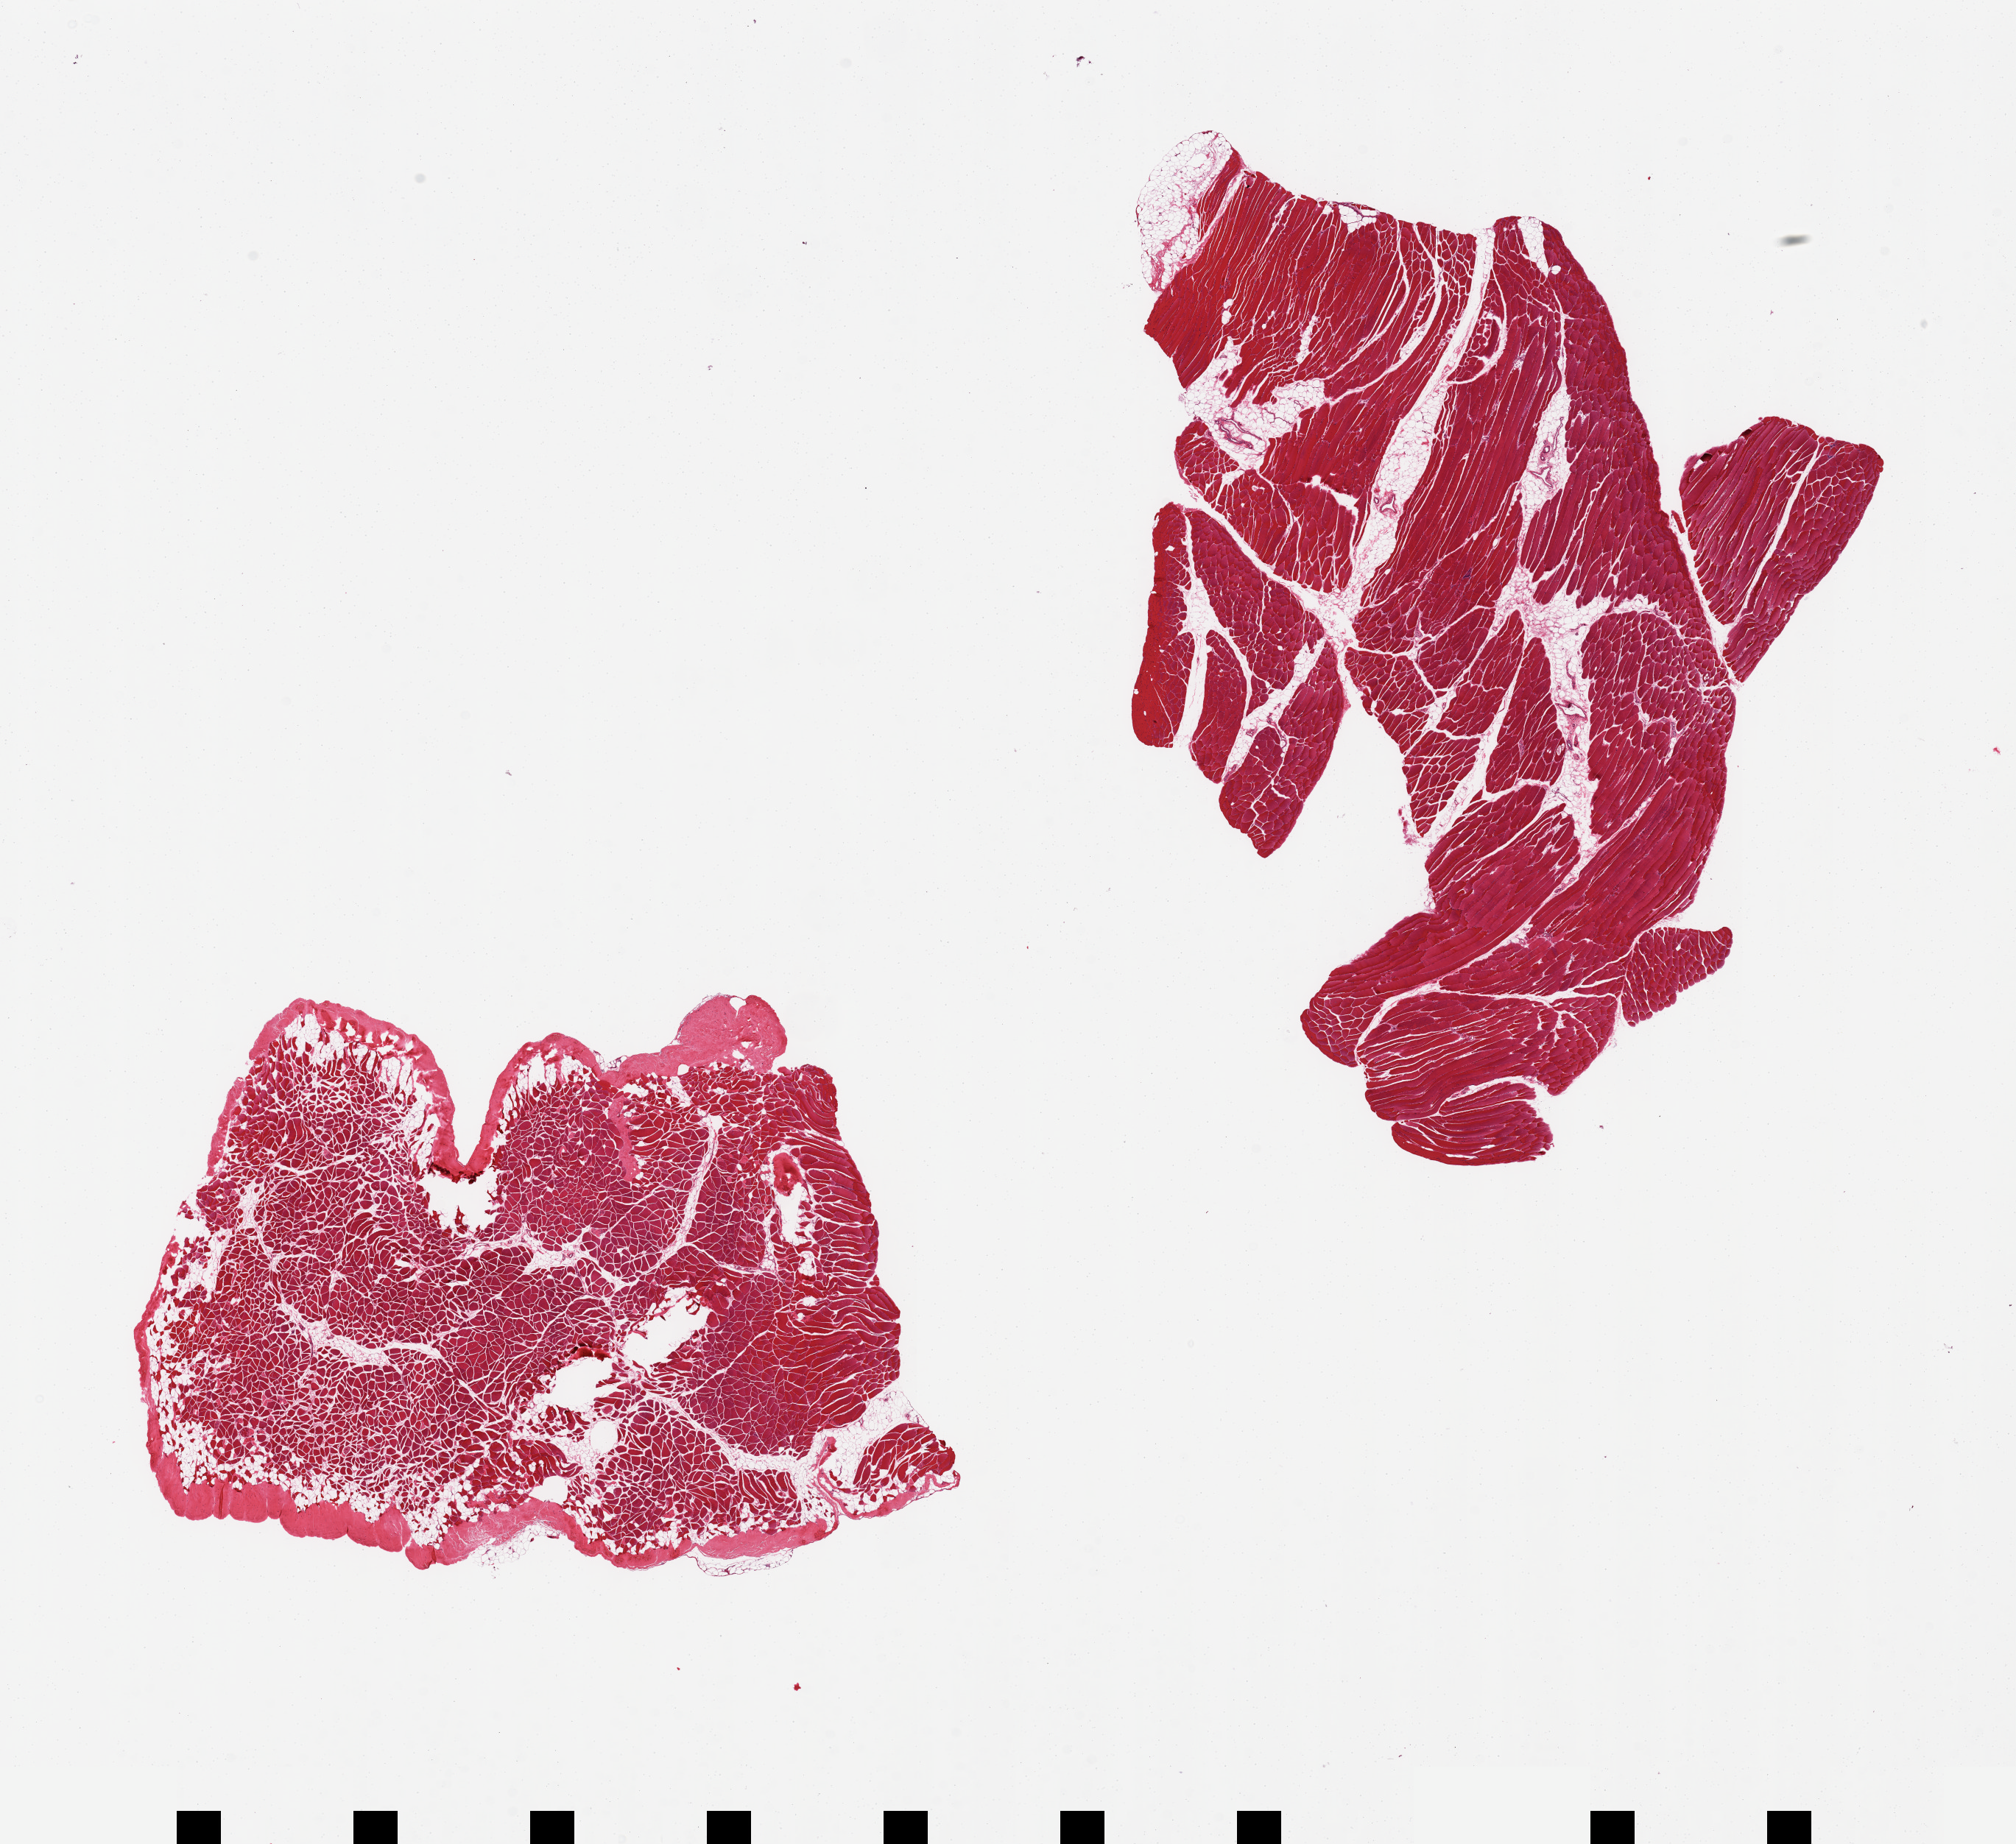
Digitized H&E-stained section, a low-resolution overview of the entire scanned area, about 21.7 x 19.8 mm (from a 20x scan), PAXgene-fixed, paraffin-embedded tissue, sampled site (target tissue): skeletal muscle, tissue donor sample. Female donor.
Review note (as recorded): 2 pieces, includes internal fat (up to 20%) and tendon.